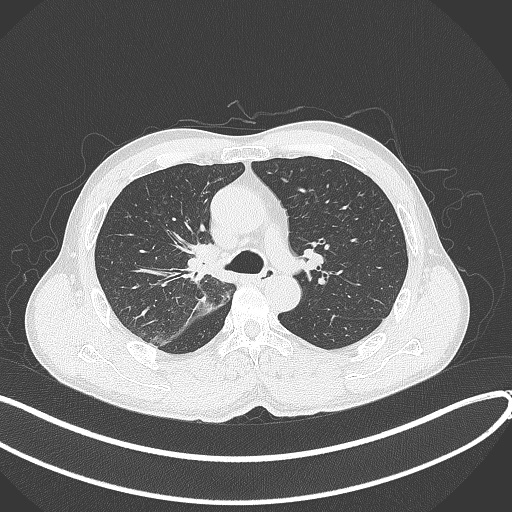
Chest CT, one axial slice; reconstruction kernel B70f; 120 kVp; lung window (W 1500 / L -600 HU); 1 mm slice thickness; 512 × 512 image matrix, field of view 400 × 400 mm. Male patient, age 53 years. From the clinical record (not read from this slice): clinical TNM (as recorded): T1b N0 M0.
Annotated regions visible in this slice (bounding box drawn by a radiologist):
- lung tumour (recorded histology: squamous cell carcinoma): box from (x=184, y=236) to (x=228, y=280) px